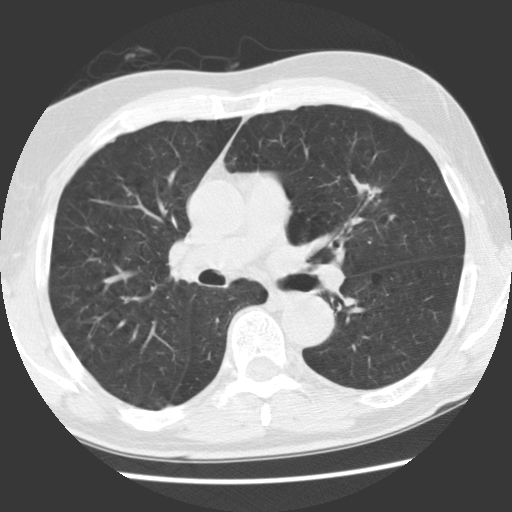
Low-dose screening chest CT, axial slice. First (baseline) screen. Lung window (W 1500 / L -600 HU). 2.5 mm slice thickness. Slice 75 of 131 in the series. Male, age 70 years at enrolment.
Expert-annotated lung lesion, box from (x=337, y=169) to (x=398, y=221) px. The screening reader recorded 2 non-calcified nodules or masses ≥4 mm on this exam; which of them this box marks is not recorded. Official screen result: positive, change unspecified: nodule(s) >= 4 mm or enlarging nodule(s), mass(es), or other non-specific abnormalities suspicious for lung cancer. Participant outcome: lung cancer diagnosed 879 days after this screen (after the third annual screen) — adenocarcinoma, NOS, left upper lobe, moderately differentiated (G2), stage IIIA (AJCC 6th edition), 17 mm at pathology.